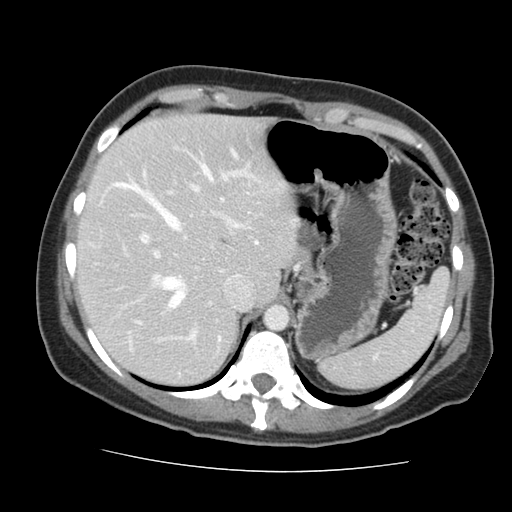
Contrast-enhanced abdominal CT, one axial slice. Slice 110 of 144 in the series (ordered by position). 120 kVp. Intravenous contrast given. Soft-tissue window (W 400 / L 40 HU). 2.5 mm slice thickness. 512 × 512 image matrix, field of view 333 × 333 mm. Female patient, age 46 years. From the clinical record (not read from this slice): diagnosis: colorectal cancer liver metastases, imaged before liver resection; multiple liver metastases: no; largest metastasis: 2.8 cm; chemotherapy before resection: yes.
Structures marked on this image (outlined manually by an expert reader):
- hepatic veins: bounding box <112,166,211,308> (left, top, right, bottom; pixels)
- liver: <80,116,294,384>
- planned liver remnant (the part of the liver to remain after resection): <80,116,294,384>
- portal vein (with intrahepatic branches): <137,171,243,341>